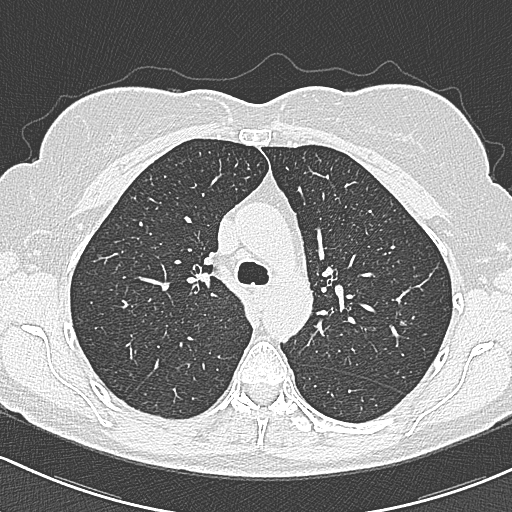
Axial slice from a low-dose chest CT screening exam; first (baseline) screen; lung window (W 1500 / L -600 HU); lung (sharp) reconstruction kernel (B80f); slice 94 of 312 in the series. Female participant, aged 65 years at enrolment. Current smoker at enrolment.
• Lesion marked by an expert reader, bounding box [x1, y1, x2, y2] px = [388, 300, 427, 337].
• The screening reader recorded 3 non-calcified nodules or masses ≥4 mm on this exam; which of them this box marks is not recorded.
• Participant outcome: lung cancer diagnosed 390 days after this screen (after the second annual screen) — bronchiolo-alveolar carcinoma, non-mucinous, left upper lobe, stage IA (AJCC 6th edition), 10 mm at pathology.